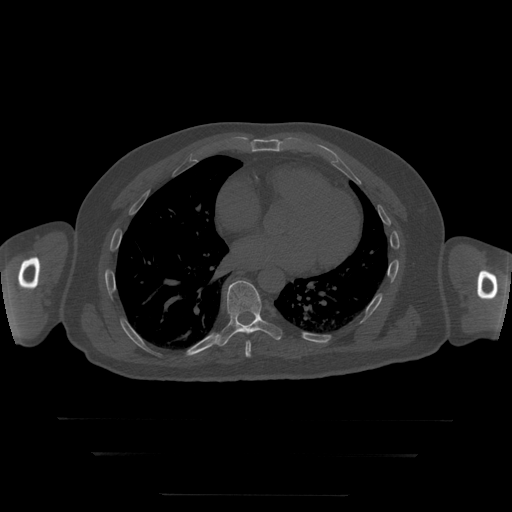
CT including the spine, one axial slice; slice 148 of 397 in the series (ordered by position); reconstruction kernel STANDARD; bone window (W 1800 / L 400 HU); 1.25 mm slice thickness; 512 × 512 image matrix, field of view 510 × 510 mm. Patient age 73 years. Case-level facts recorded for this patient, not image findings: primary cancer: prostate.
Annotated regions visible in this slice (semi-automatically segmented with operator editing):
- T8 vertebra: bounding box <245,341,251,358> (left, top, right, bottom; pixels)
- T9 vertebra: <215,281,282,347>